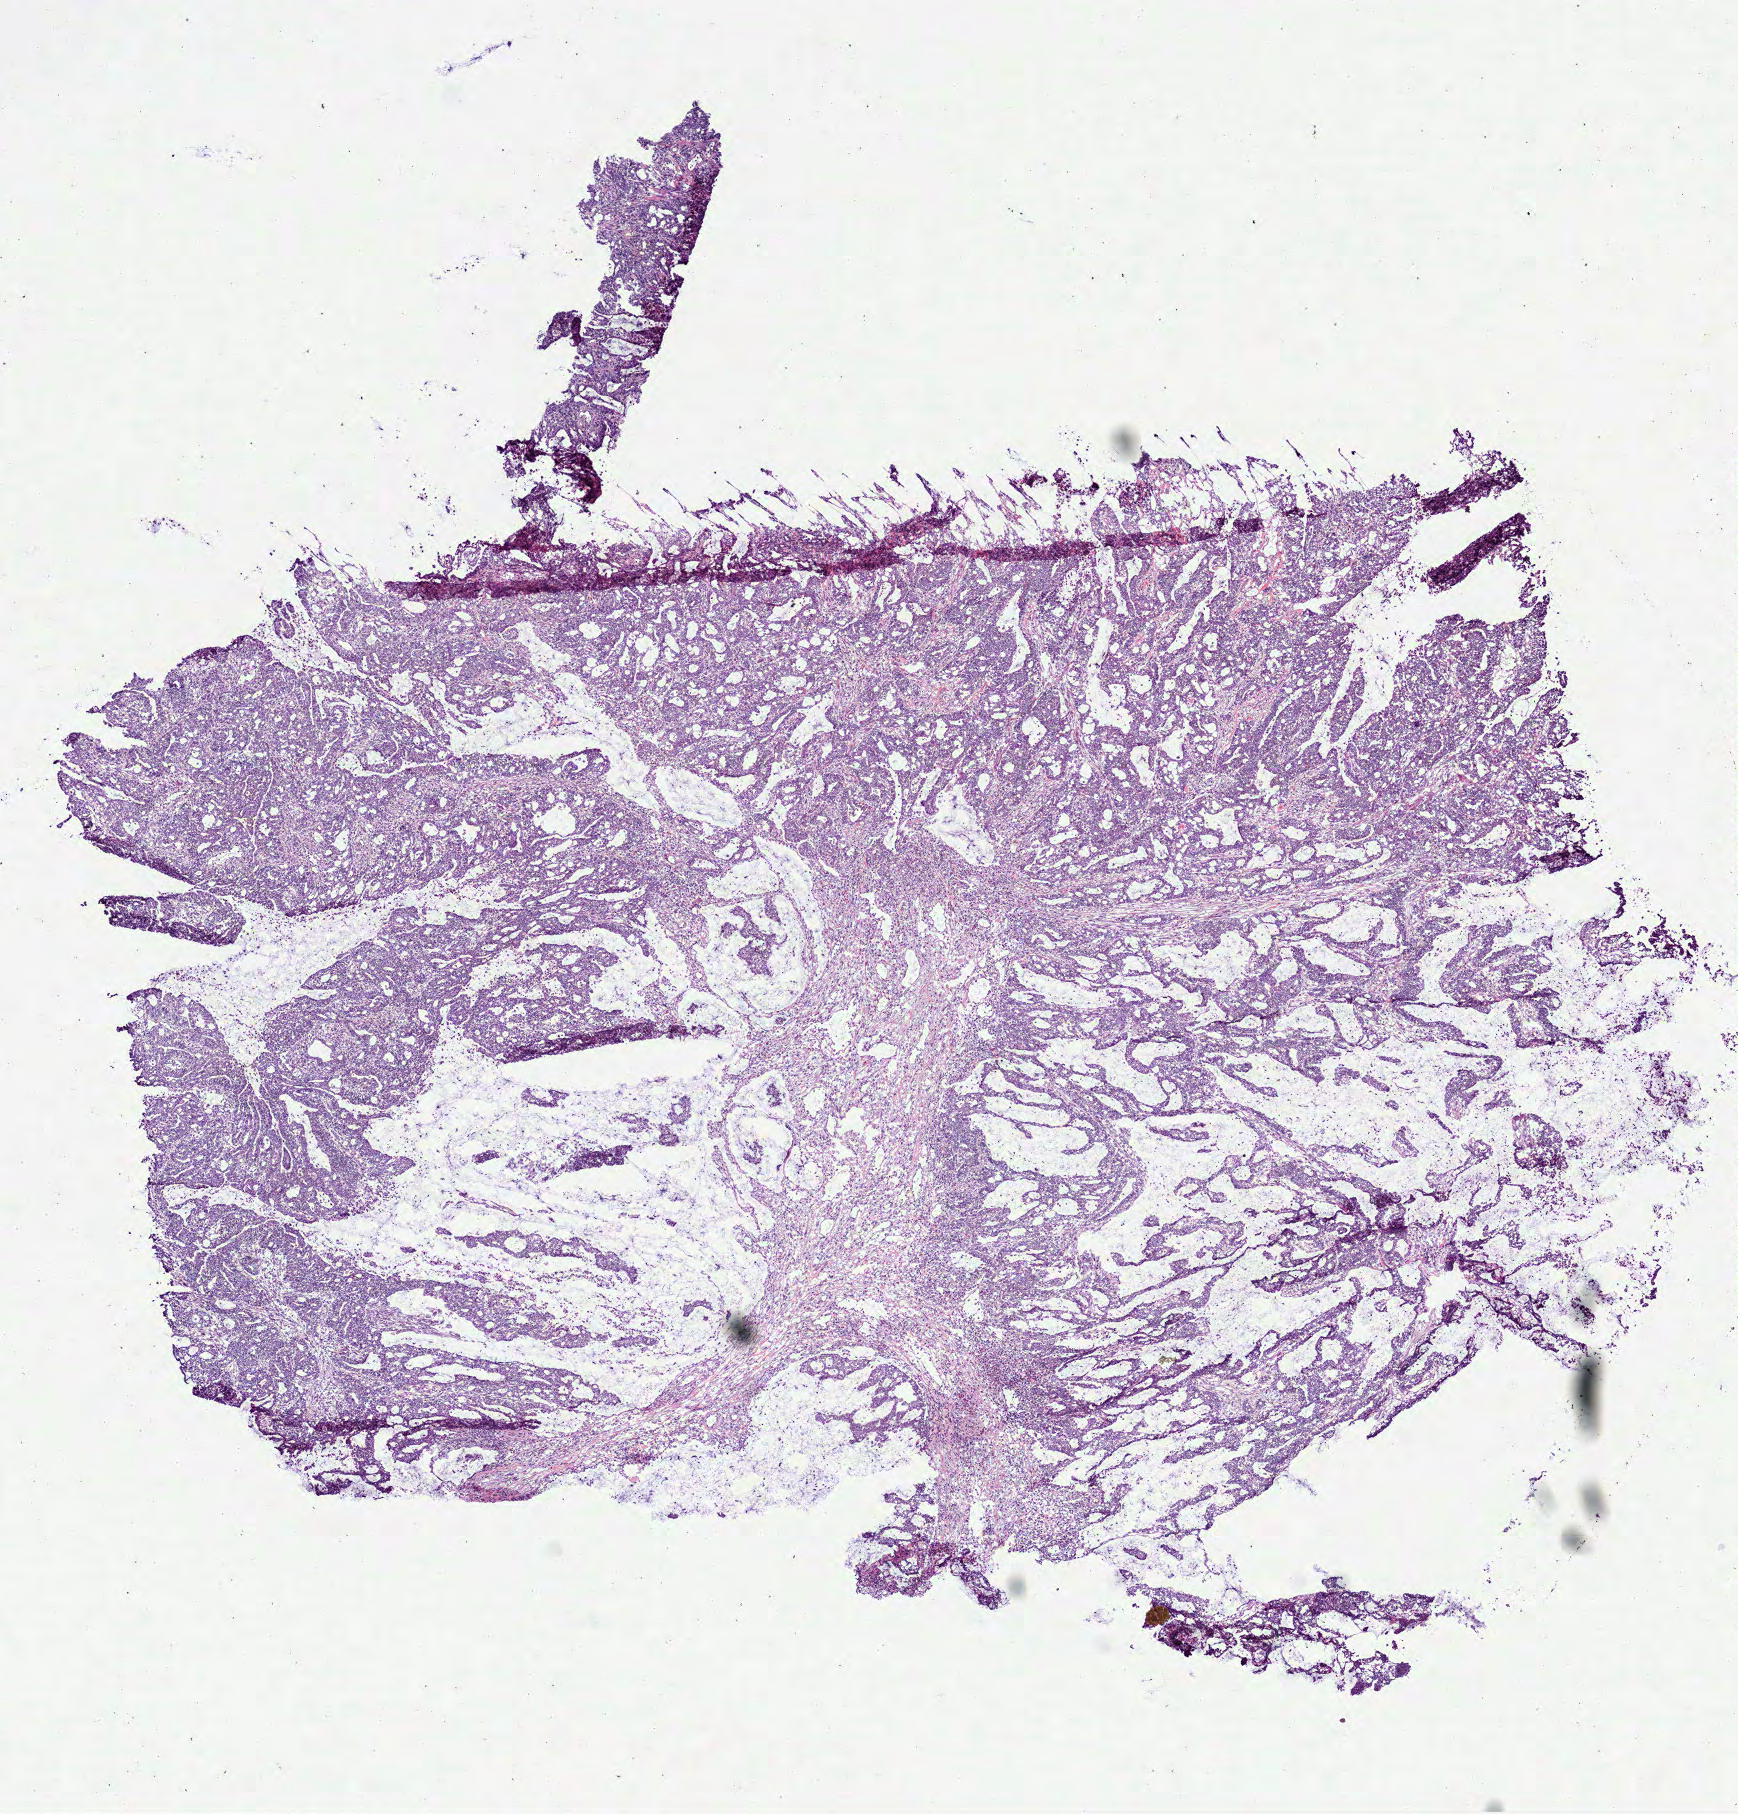
H&E whole-slide image, whole scanned area (about 7.0 x 7.3 mm) shown as a low-resolution overview, frozen section from the bottom of the tissue portion, primary tumour sample from the colon. Male, age 66 years at initial diagnosis. Pathologist review of this section (percent, as recorded): tumour cells 100%, tumour nuclei 80%, normal cells 0%, stromal cells 0%, necrosis 0%. Inflammatory infiltration, as recorded: lymphocyte infiltration 8%, monocyte infiltration 2%, neutrophil infiltration 8%.
AJCC pathologic stage: I. Pathologic diagnosis: Mucinous adenocarcinoma (cecum). Lymph nodes positive (case pathology): 0 of 13 examined.